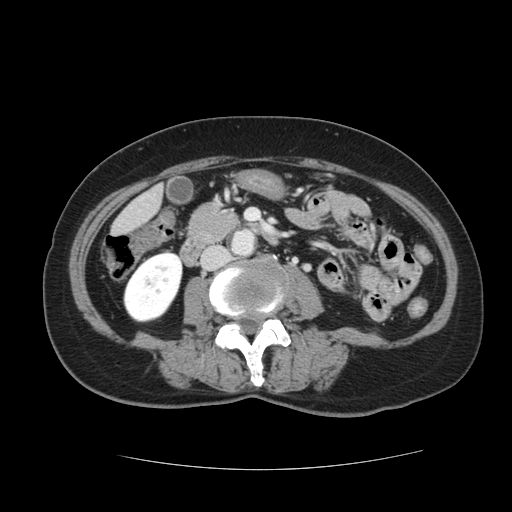
Contrast-enhanced abdominal CT, one axial slice; slice 18 of 128 in the series (ordered by position); intravenous contrast given; soft-tissue window (W 400 / L 40 HU); 2.5 mm slice thickness; 512 × 512 image matrix, field of view 366 × 366 mm. Female patient, age 67 years. Case-level facts recorded for this patient, not image findings: diagnosis: colorectal cancer liver metastases, imaged before liver resection; multiple liver metastases: yes; largest metastasis: 3 cm; disease in both lobes: yes.
Annotated regions visible in this slice (manually delineated by an expert):
- liver: box from (x=114, y=189) to (x=161, y=236) px
- planned liver remnant (the part of the liver to remain after resection): (x=113, y=206)–(x=144, y=236)